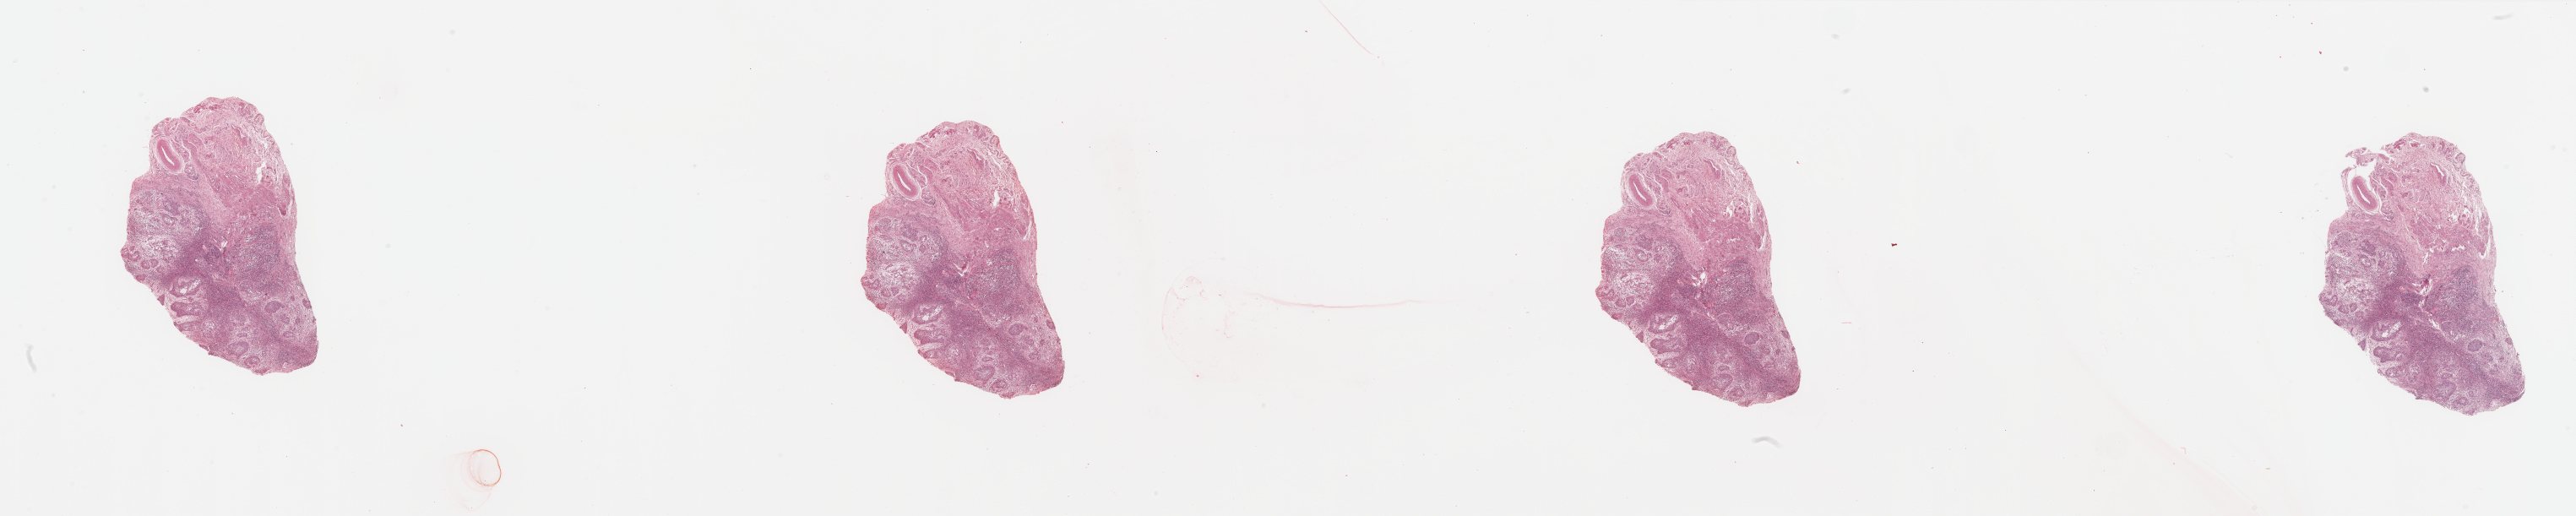
H&E whole-slide image, a low-resolution overview of the entire scanned area, about 48.2 x 9.7 mm (from a 20x scan), head and neck, tissue type not recorded. Male, 60 y/o.
* patient diagnosis: Squamous cell carcinoma, NOS (larynx, NOS)